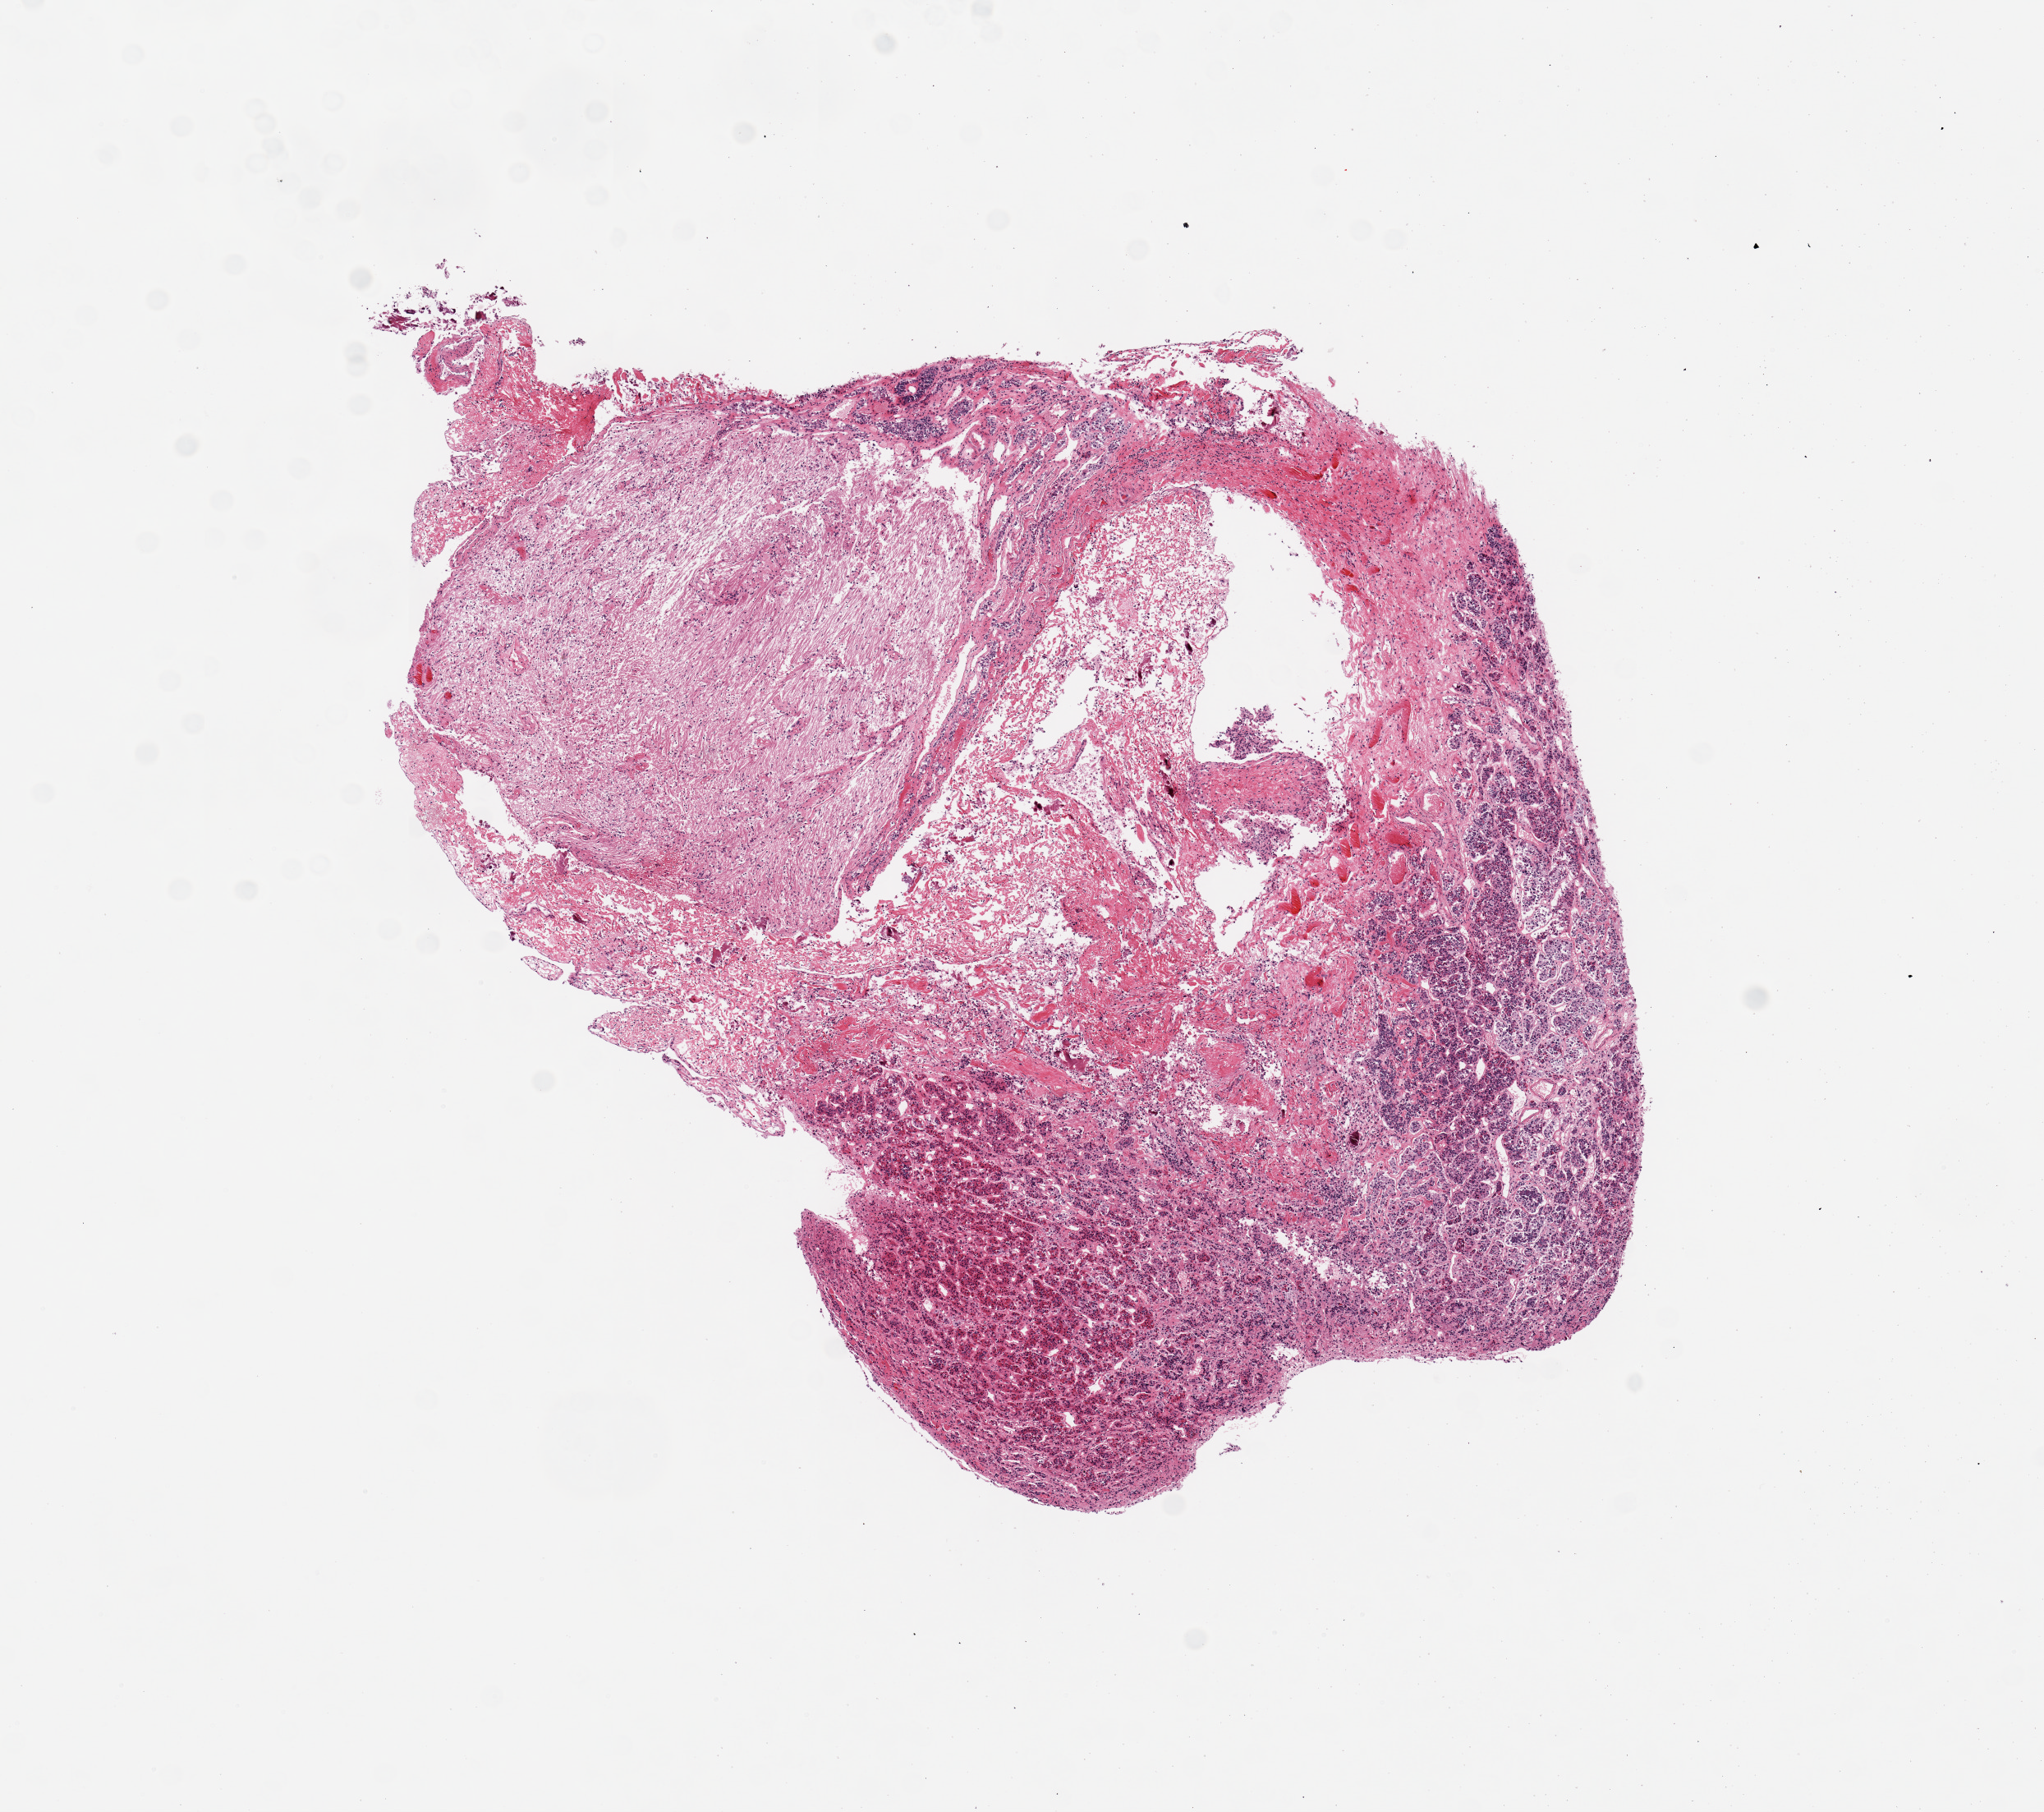
Digitized H&E-stained section, a low-resolution overview of the entire scanned area, about 9.8 x 8.7 mm (slide scanned at 20x), PAXgene-fixed paraffin-embedded (PFPE) section, section of pituitary (target tissue), tissue donor sample.
Reviewer comment on this tissue sample: 1 piece; anterior, posterior and intermediate zones.